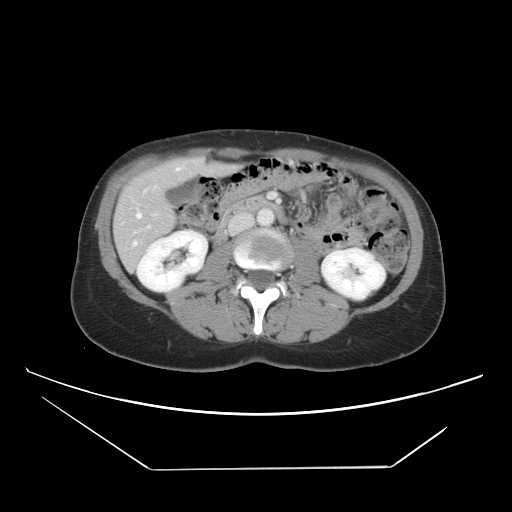
Contrast-enhanced abdominal CT, one axial slice. Slice 16 of 42 in the series (ordered by position). 120 kVp. Soft-tissue window (W 400 / L 40 HU). 512 × 512 image matrix. Female patient, age 52 years. From the clinical record (not read from this slice): diagnosis: colorectal cancer liver metastases, imaged before liver resection.
Structures marked on this image (outlined manually by an expert reader):
- hepatic veins: bounding box <132,161,201,246> (left, top, right, bottom; pixels)
- liver: <116,158,232,269>
- planned liver remnant (the part of the liver to remain after resection): <121,158,215,215>
- portal vein (with intrahepatic branches): <143,189,270,229>